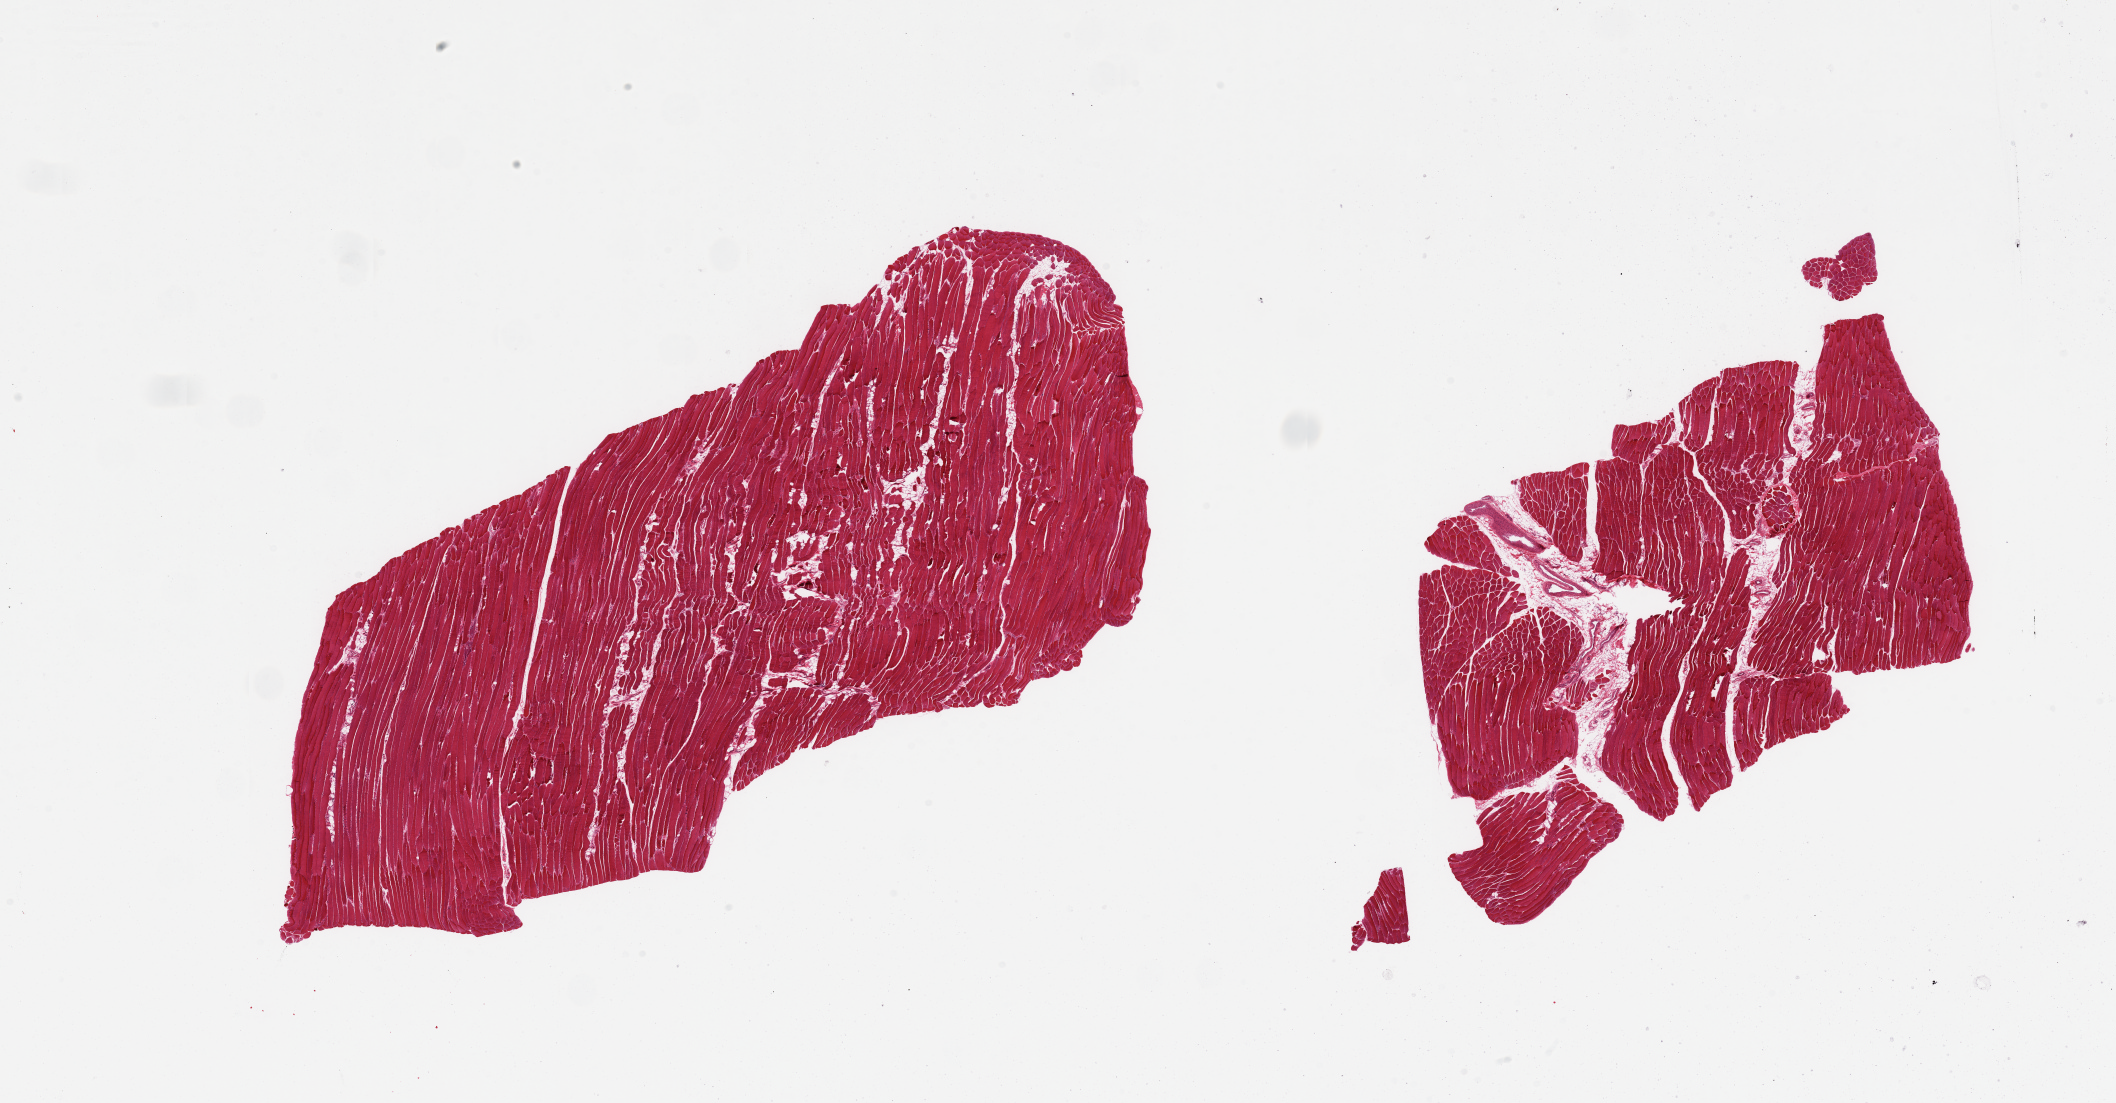
Hematoxylin and eosin (H&E) whole-slide image, whole scanned area (about 33.5 x 17.4 mm, slide scanned at 20x) shown as a low-resolution overview, PAXgene-fixed paraffin-embedded (PFPE) section, section of skeletal muscle (target tissue), donor tissue sample. Donor: female.
* pathologist's review note for this sample: 2 pieces